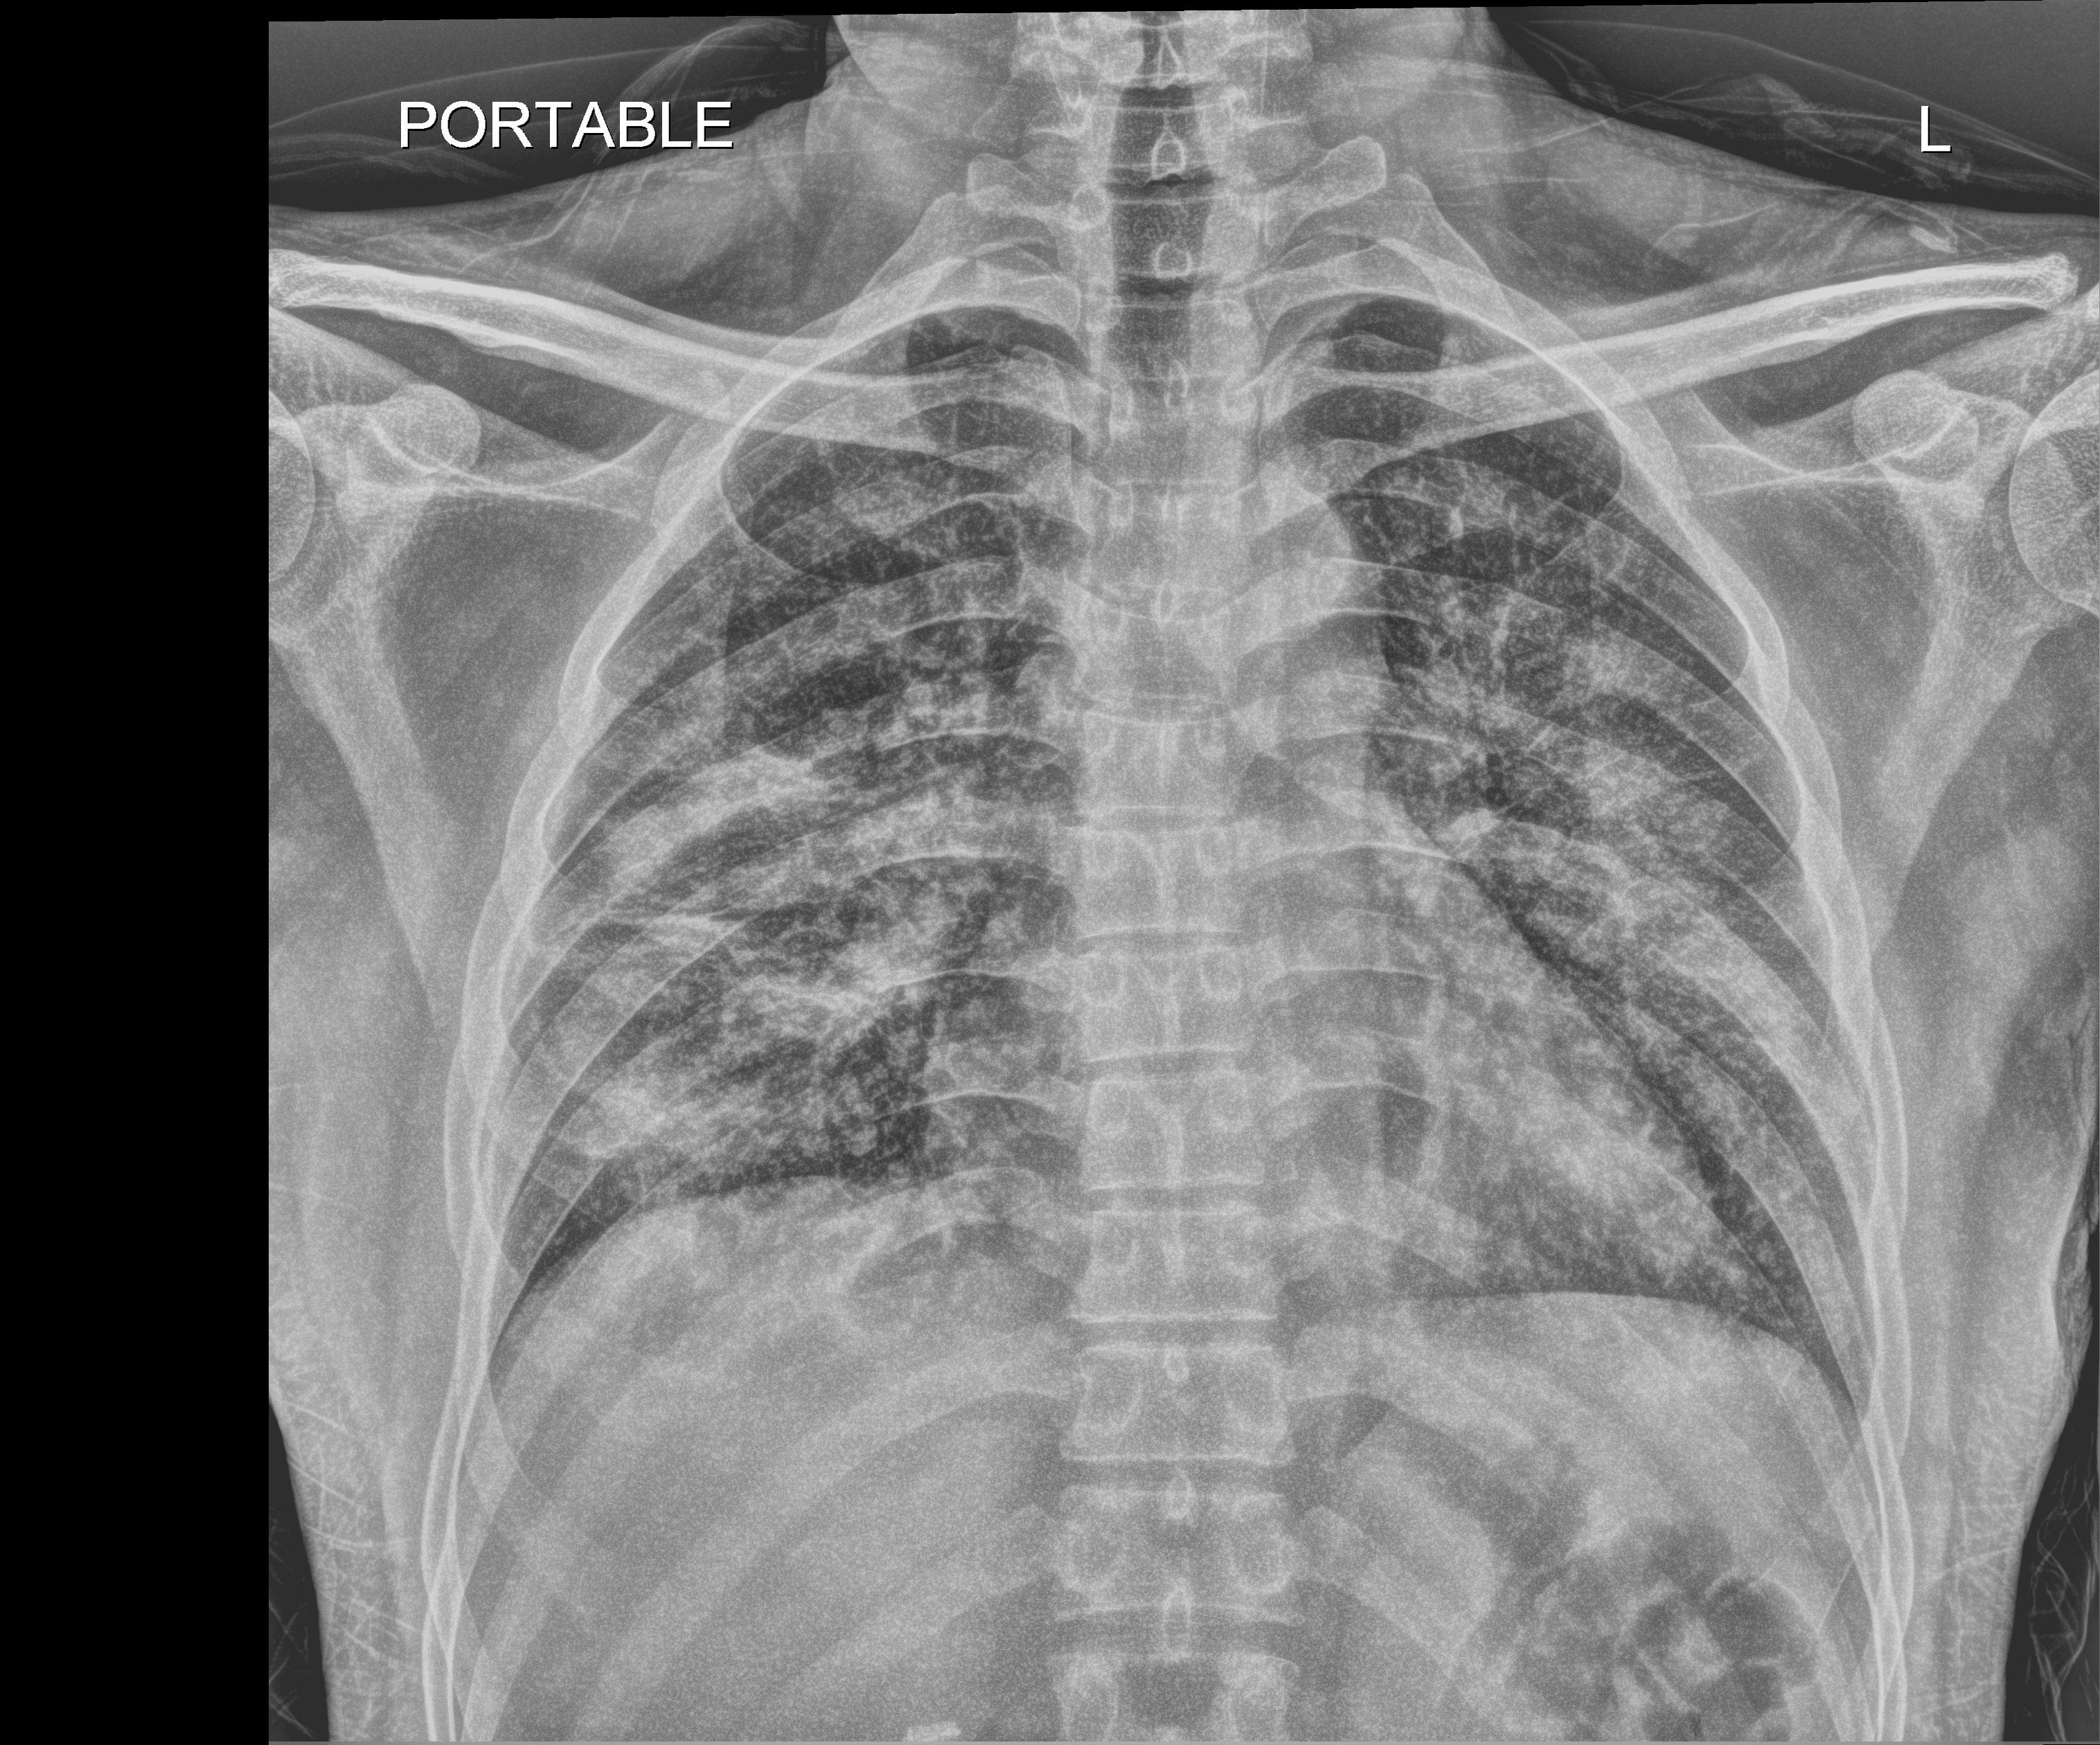
Chest radiograph; anteroposterior (AP) projection. Male patient hospitalised with COVID-19, age 18–59 years.
Hospital-stay facts (about this admission, not read from this image; timing relative to this image not recorded): other chronic lung disease (admission record): no; smoking status (admission record): never.